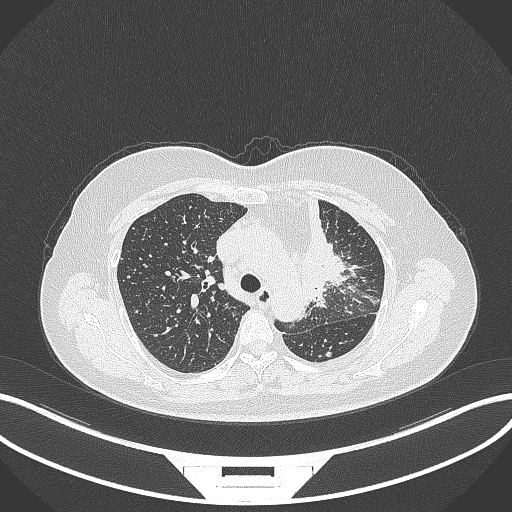
Chest CT, one axial slice. Reconstruction kernel B70f. Lung window (W 1500 / L -600 HU). 1 mm slice thickness. 512 × 512 image matrix. Female patient, age 49 years. From the clinical record (not read from this slice): clinical TNM (as recorded): T1c N0 M1.
Annotated regions visible in this slice (rectangle marked by the reading radiologist):
- lung tumour (recorded histology: adenocarcinoma): box from (x=293, y=198) to (x=349, y=310) px